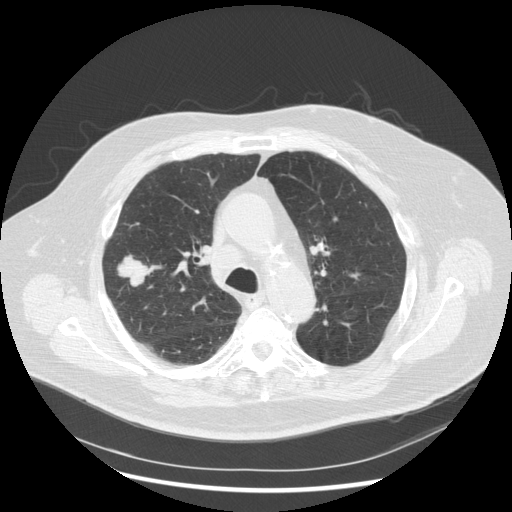
Low-dose screening chest CT, one axial slice; slice 191 of 263 in the series (ordered by position); reconstruction kernel STANDARD; 120 kVp; lung window (W 1500 / L -600 HU); 512 × 512 image matrix, field of view 400 × 400 mm.
Outlined on this slice (manually delineated by an expert):
- lesion 1 (tumor, upper lobe of right lung): bounding box (x1, y1, x2, y2) in pixels: (118, 255, 148, 286)